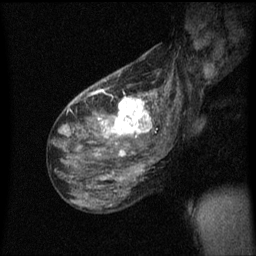
Breast MRI (dynamic contrast-enhanced), one sagittal slice. Slice 34 of 60 in the series (ordered by position). Dynamic contrast-enhanced series, image 2 of 3 at this slice position (ordered by acquisition). 1.5 T. TE 4.2 ms, TR 8.4 ms. 256 × 256 image matrix, field of view 200 × 200 mm. Patient: female, 49 years.
Structures marked on this image (semi-automatic segmentation, software-assisted and operator-edited):
- analysis volume of interest (the breast-tissue region the enhancement analysis was run in; not a lesion): bounding box (x1, y1, x2, y2) in pixels: (103, 90, 157, 151)
- tumour enhancement mask (voxels above the 70 % enhancement threshold inside the analysis volume of interest): (103, 90, 154, 151)